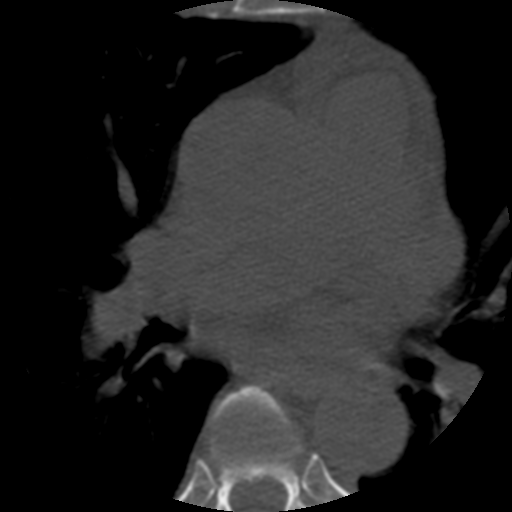
CT including the spine, one axial slice. Slice 363 of 508 in the series (ordered by position). Reconstruction kernel STANDARD. 120 kVp. Bone window (W 1800 / L 400 HU). 1.25 mm slice thickness. 512 × 512 image matrix, field of view 160 × 160 mm. Patient age 57 years. From the clinical record (not read from this slice): primary cancer: prostate.
Outlined on this slice (semi-automatically segmented with operator editing):
- T5 vertebra: bounding box [x1, y1, x2, y2] px = [211, 388, 301, 465]
- T6 vertebra: [212, 386, 311, 512]